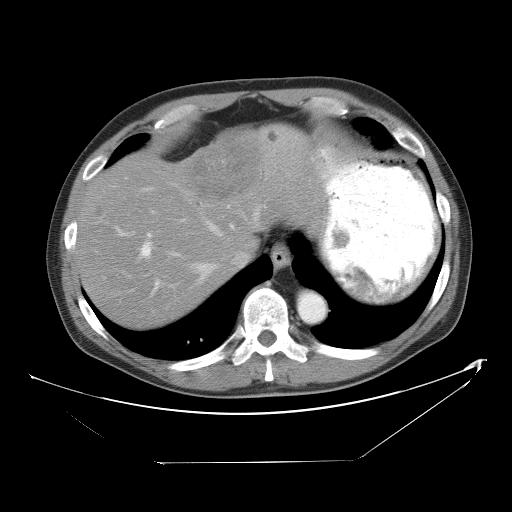
Contrast-enhanced abdominal CT, one axial slice; slice 43 of 53 in the series (ordered by position); reconstruction kernel STANDARD; soft-tissue window (W 400 / L 40 HU); 512 × 512 image matrix, field of view 438 × 438 mm. Male patient, age 59 years. From the clinical record (not read from this slice): diagnosis: colorectal cancer liver metastases, imaged before liver resection; multiple liver metastases: yes; largest metastasis: 8.5 cm; disease in both lobes: no.
Annotated regions visible in this slice (manually delineated by an expert):
- hepatic veins: bounding box [x1, y1, x2, y2] px = [170, 205, 262, 280]
- liver: [77, 126, 324, 328]
- planned liver remnant (the part of the liver to remain after resection): [77, 164, 230, 328]
- portal vein (with intrahepatic branches): [116, 211, 234, 289]
- liver metastasis: [98, 209, 103, 217]
- liver metastasis: [270, 132, 278, 142]
- liver metastasis: [192, 134, 254, 202]